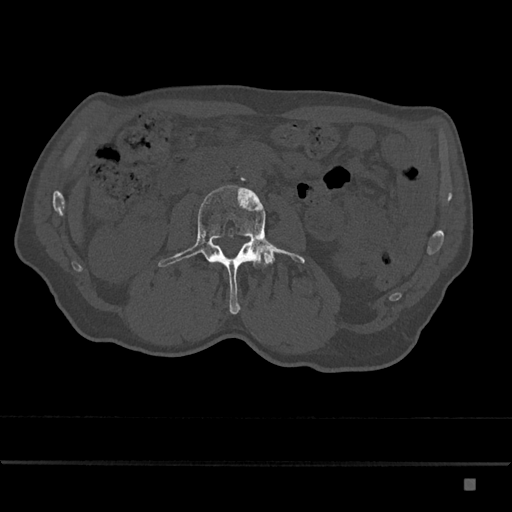
CT including the spine, one axial slice. Position 409 of 797 along the scan axis. 120 kVp. Bone window (W 1800 / L 400 HU). 512 × 512 image matrix. Male patient, age 72 years. Case-level facts recorded for this patient, not image findings: primary cancer: prostate.
Annotated regions visible in this slice (semi-automatic segmentation, software-assisted and operator-edited):
- L3 vertebra: bounding box <158,185,305,314> (left, top, right, bottom; pixels)
- L4 vertebra: <263,255,271,266>